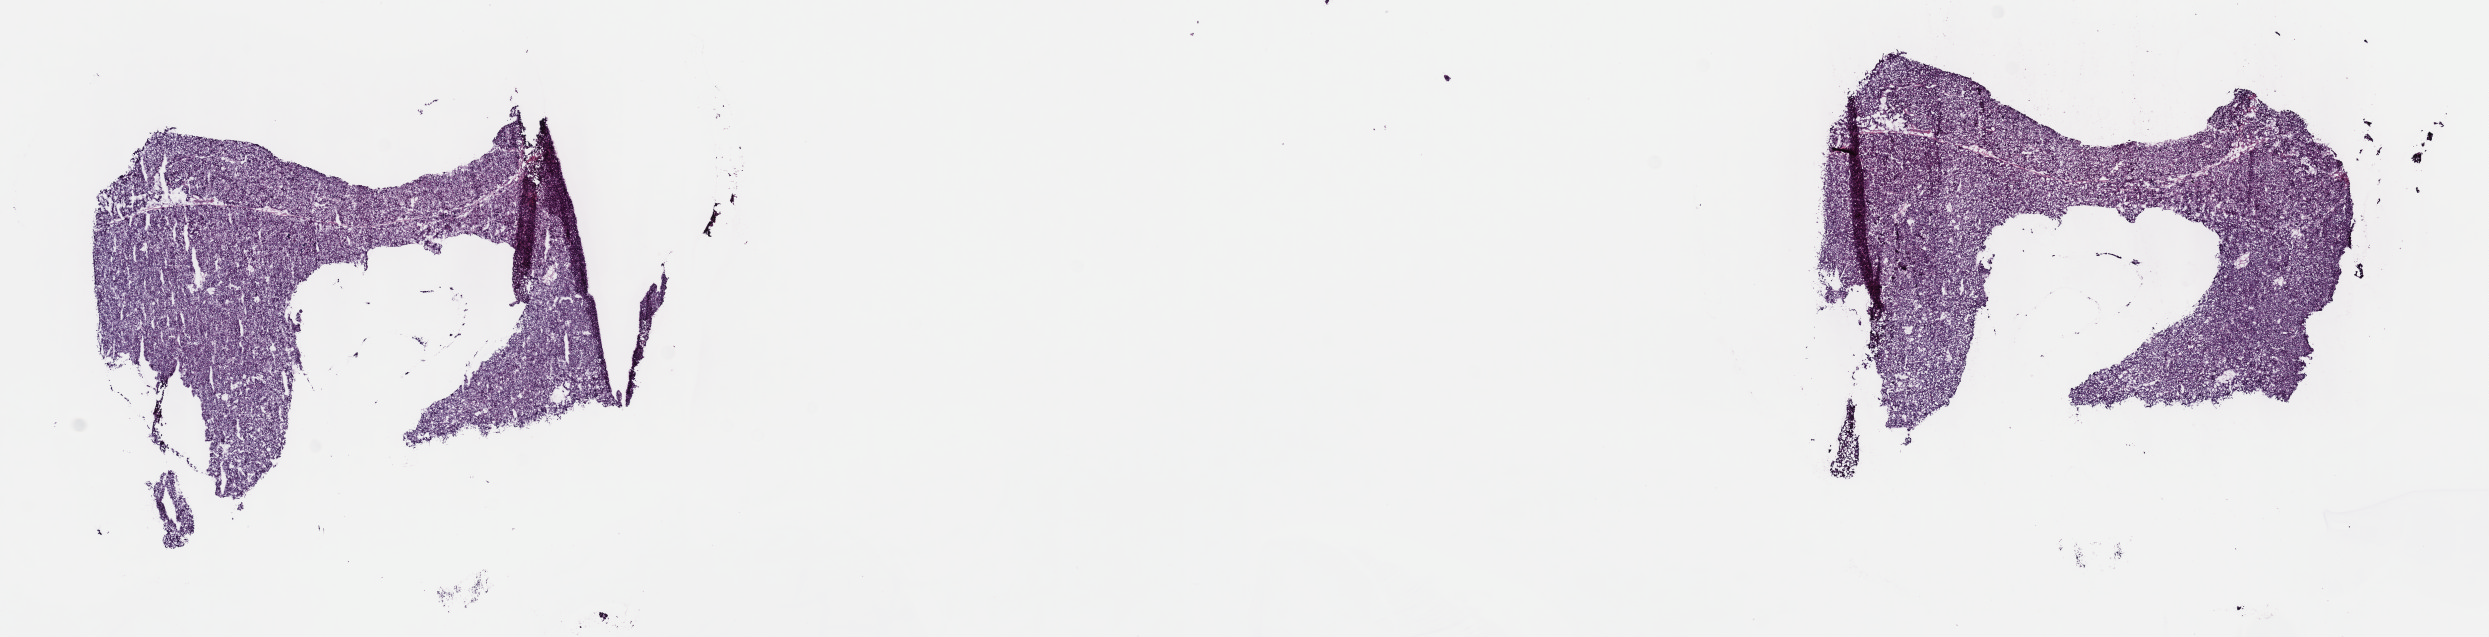
H&E whole-slide image — low-resolution overview of the scanned area, about 20.1 x 5.2 mm, frozen section from the top of the tissue portion, liver, primary tumour sample. Male patient; age at initial diagnosis 53 years. Histologic grade: G3 (poorly differentiated). Pathologist review of this section (percent, as recorded): tumour cells 100%, tumour nuclei 95%, normal cells 0%, stromal cells 0%, necrosis 0%. Infiltration values recorded for this section: lymphocyte infiltration 0%, monocyte infiltration 0%, neutrophil infiltration 0%.
AJCC pathologic stage: I (7th edition). TNM: T1 N0 M0. Histologic diagnosis: Hepatocellular carcinoma, NOS.